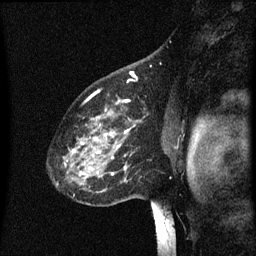
Breast MRI (dynamic contrast-enhanced), one sagittal slice; position 45 of 60 along the scan axis; dynamic contrast-enhanced series, image 2 of 3 at this slice position (ordered by acquisition); 1.5 T; TE 4.2 ms, TR 8 ms; 2 mm slice thickness; 256 × 256 image matrix. Patient: female, 60 years.
Structures marked on this image (semi-automatically segmented with operator editing):
- analysis volume of interest (the breast-tissue region the enhancement analysis was run in; not a lesion): bounding box [x1, y1, x2, y2] px = [49, 96, 142, 197]
- tumour enhancement mask (voxels above the 70 % enhancement threshold inside the analysis volume of interest): [65, 100, 131, 177]